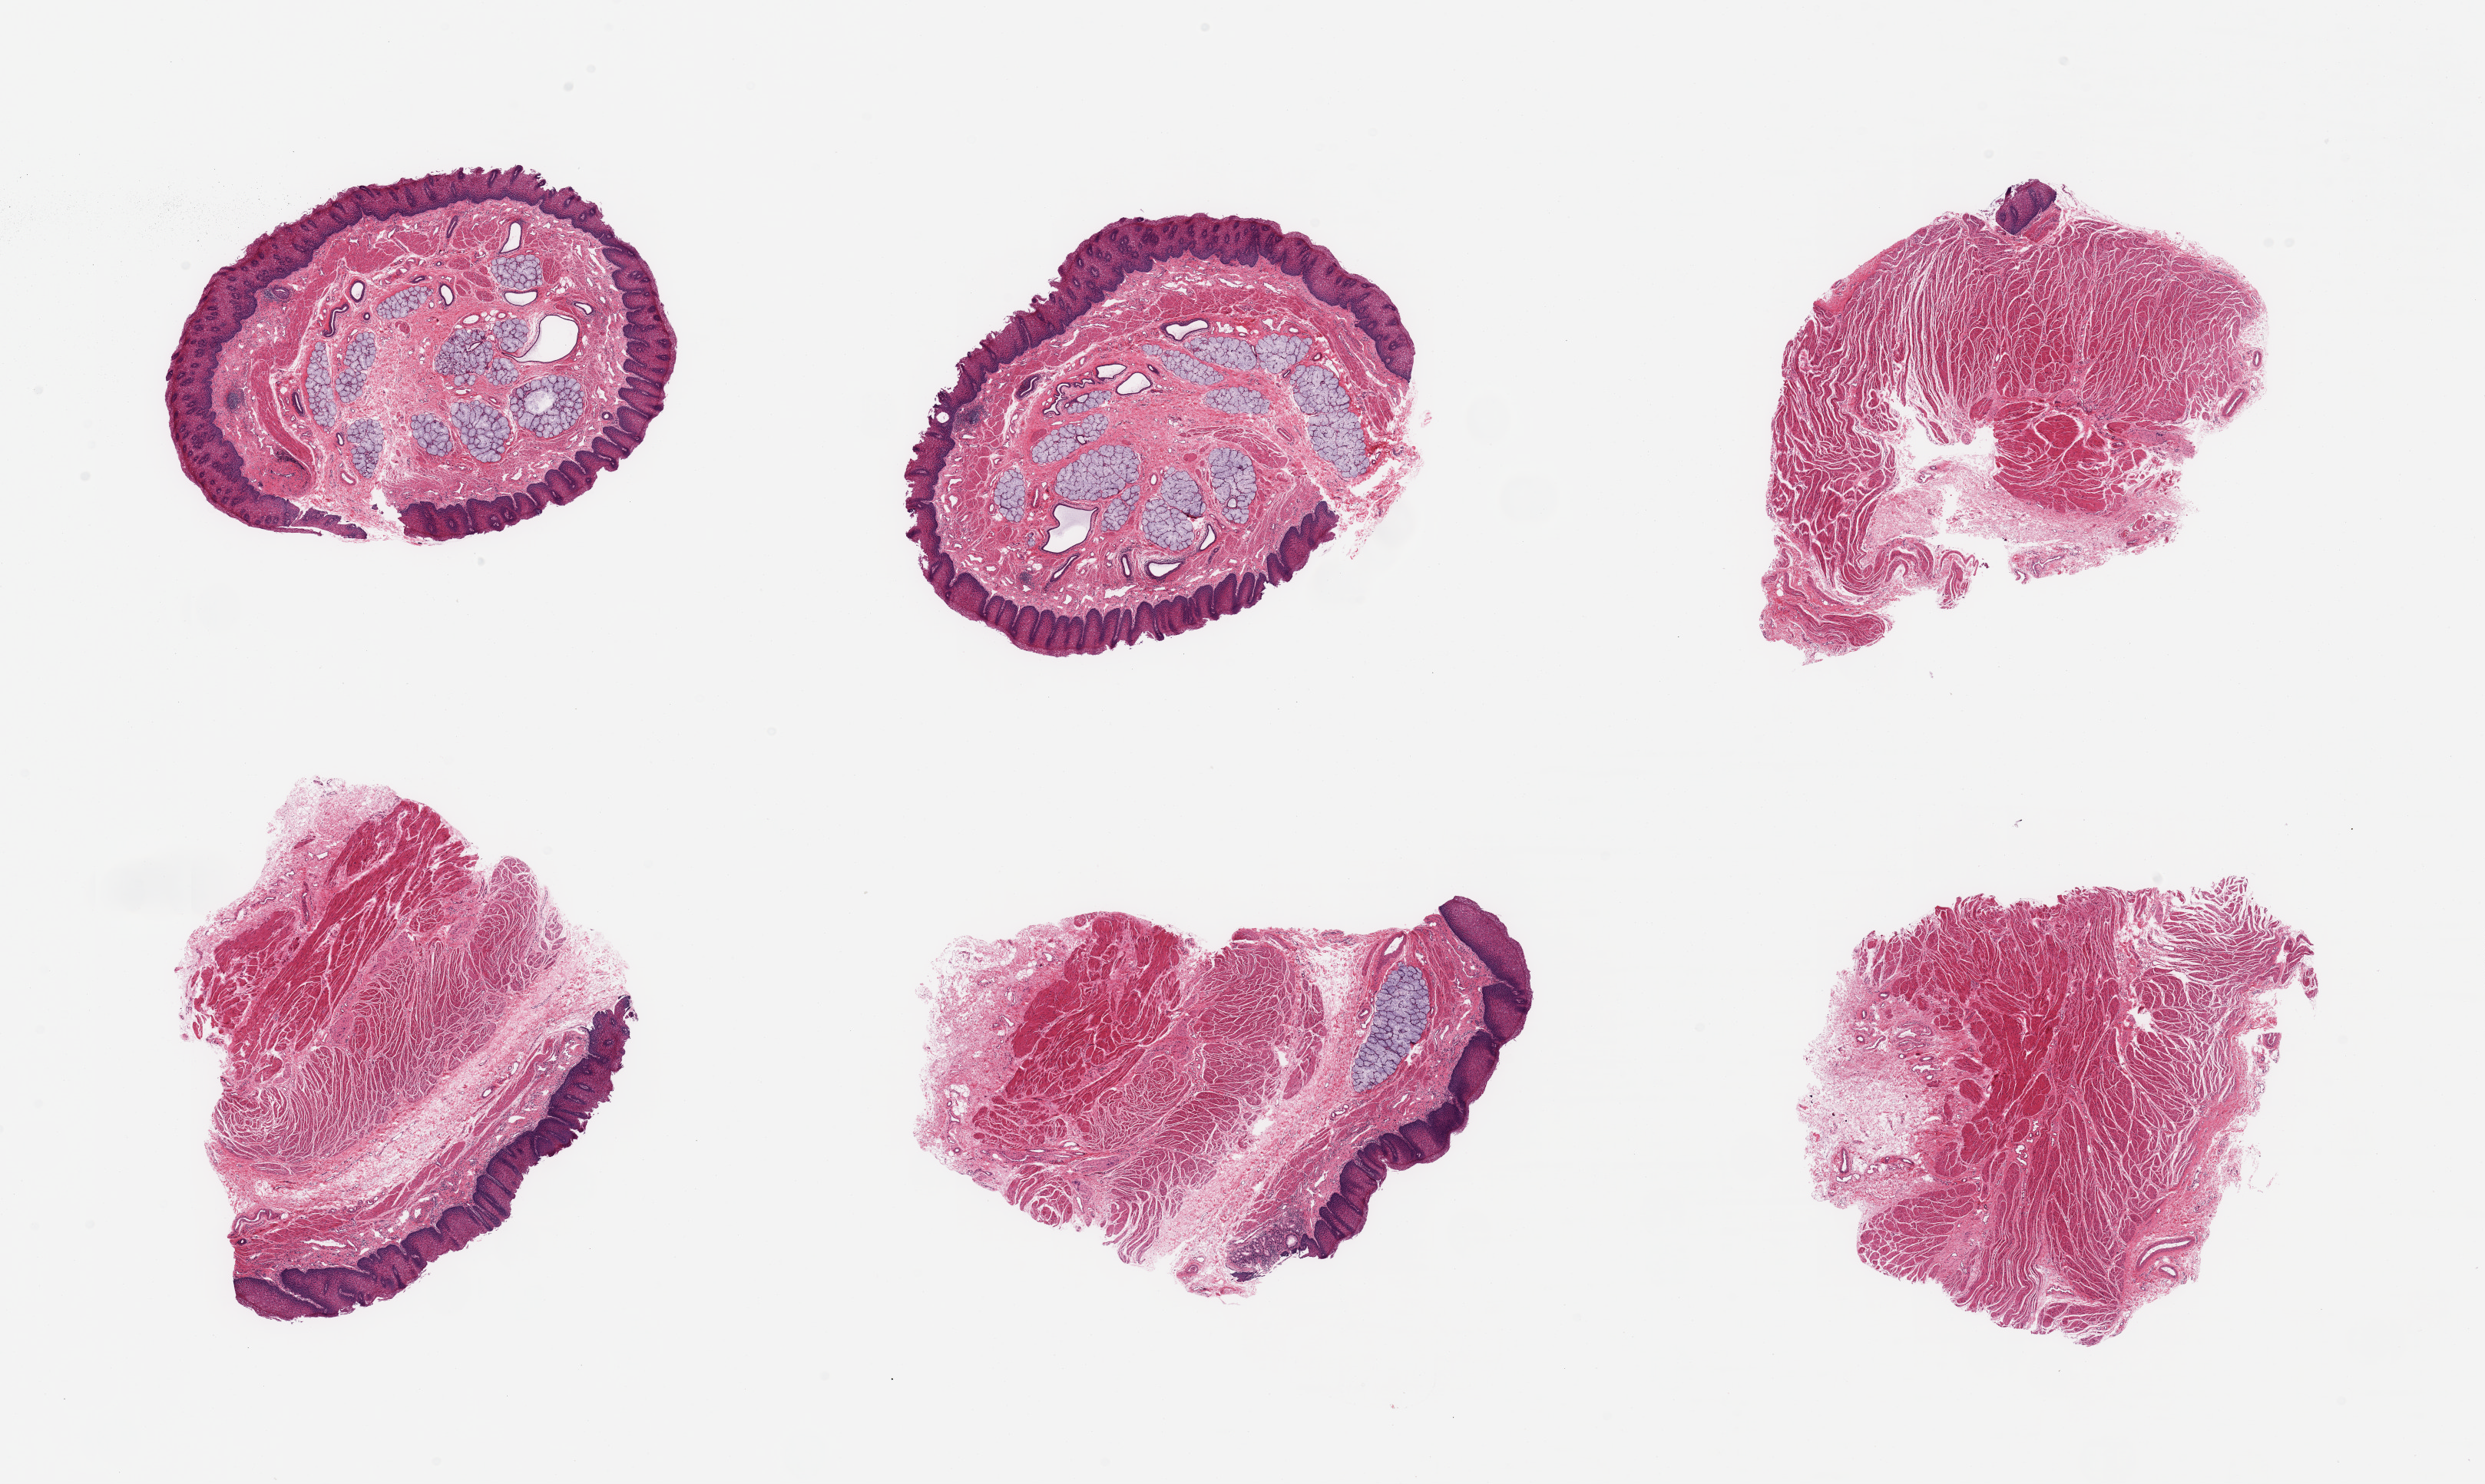
Whole-slide image, hematoxylin and eosin (H&E) stain — shown as a low-resolution overview of the whole scanned area (about 25.6 x 15.3 mm), PAXgene-fixed paraffin-embedded (PFPE) section, sampled site (target tissue): gastroesophageal junction, donor tissue sample. Male donor.
Reviewer comment on this tissue sample: 6 pieces; 4 contain squamous mucosa and 3 contain submucosal glands; 4 contain target muscularis.